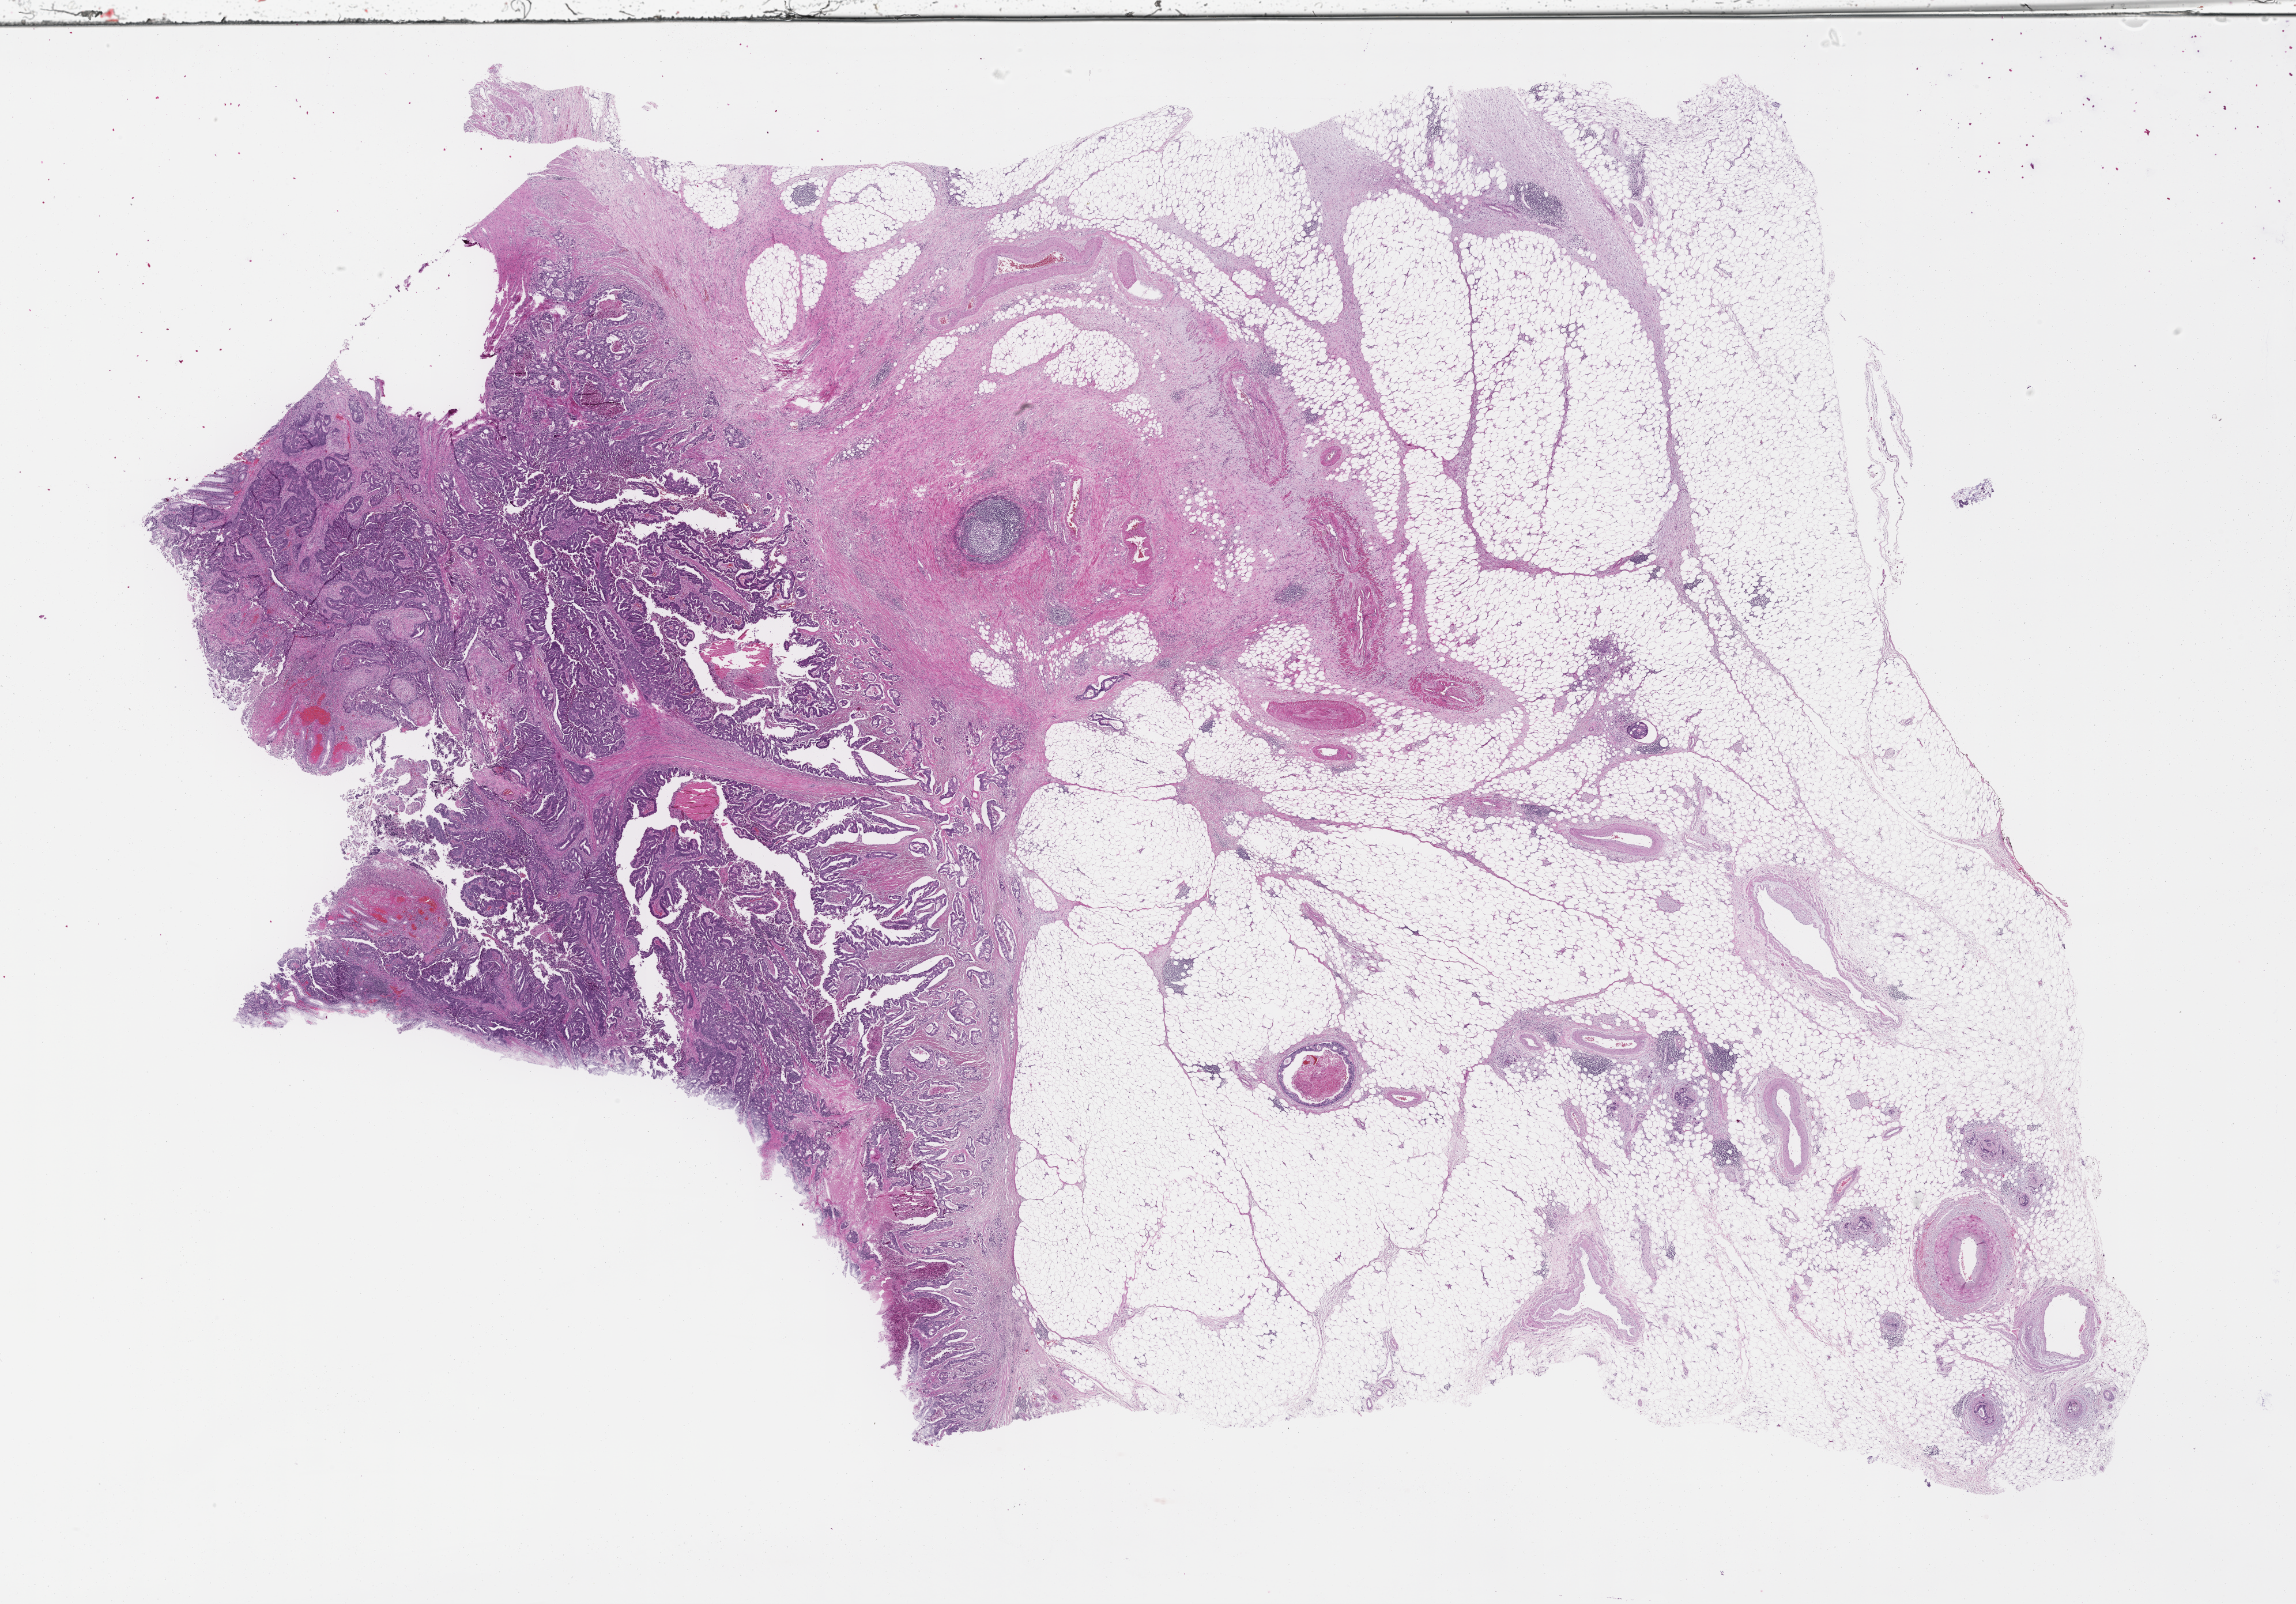
Digitized hematoxylin and eosin (H&E)-stained section — whole scanned area (about 32.2 x 22.5 mm) shown as a low-resolution overview. FFPE section. Tissue site: colon. Specimen time point: archival tissue. Patient: male.
This section: primary tumor. Diagnosis: Colorectal Carcinoma.